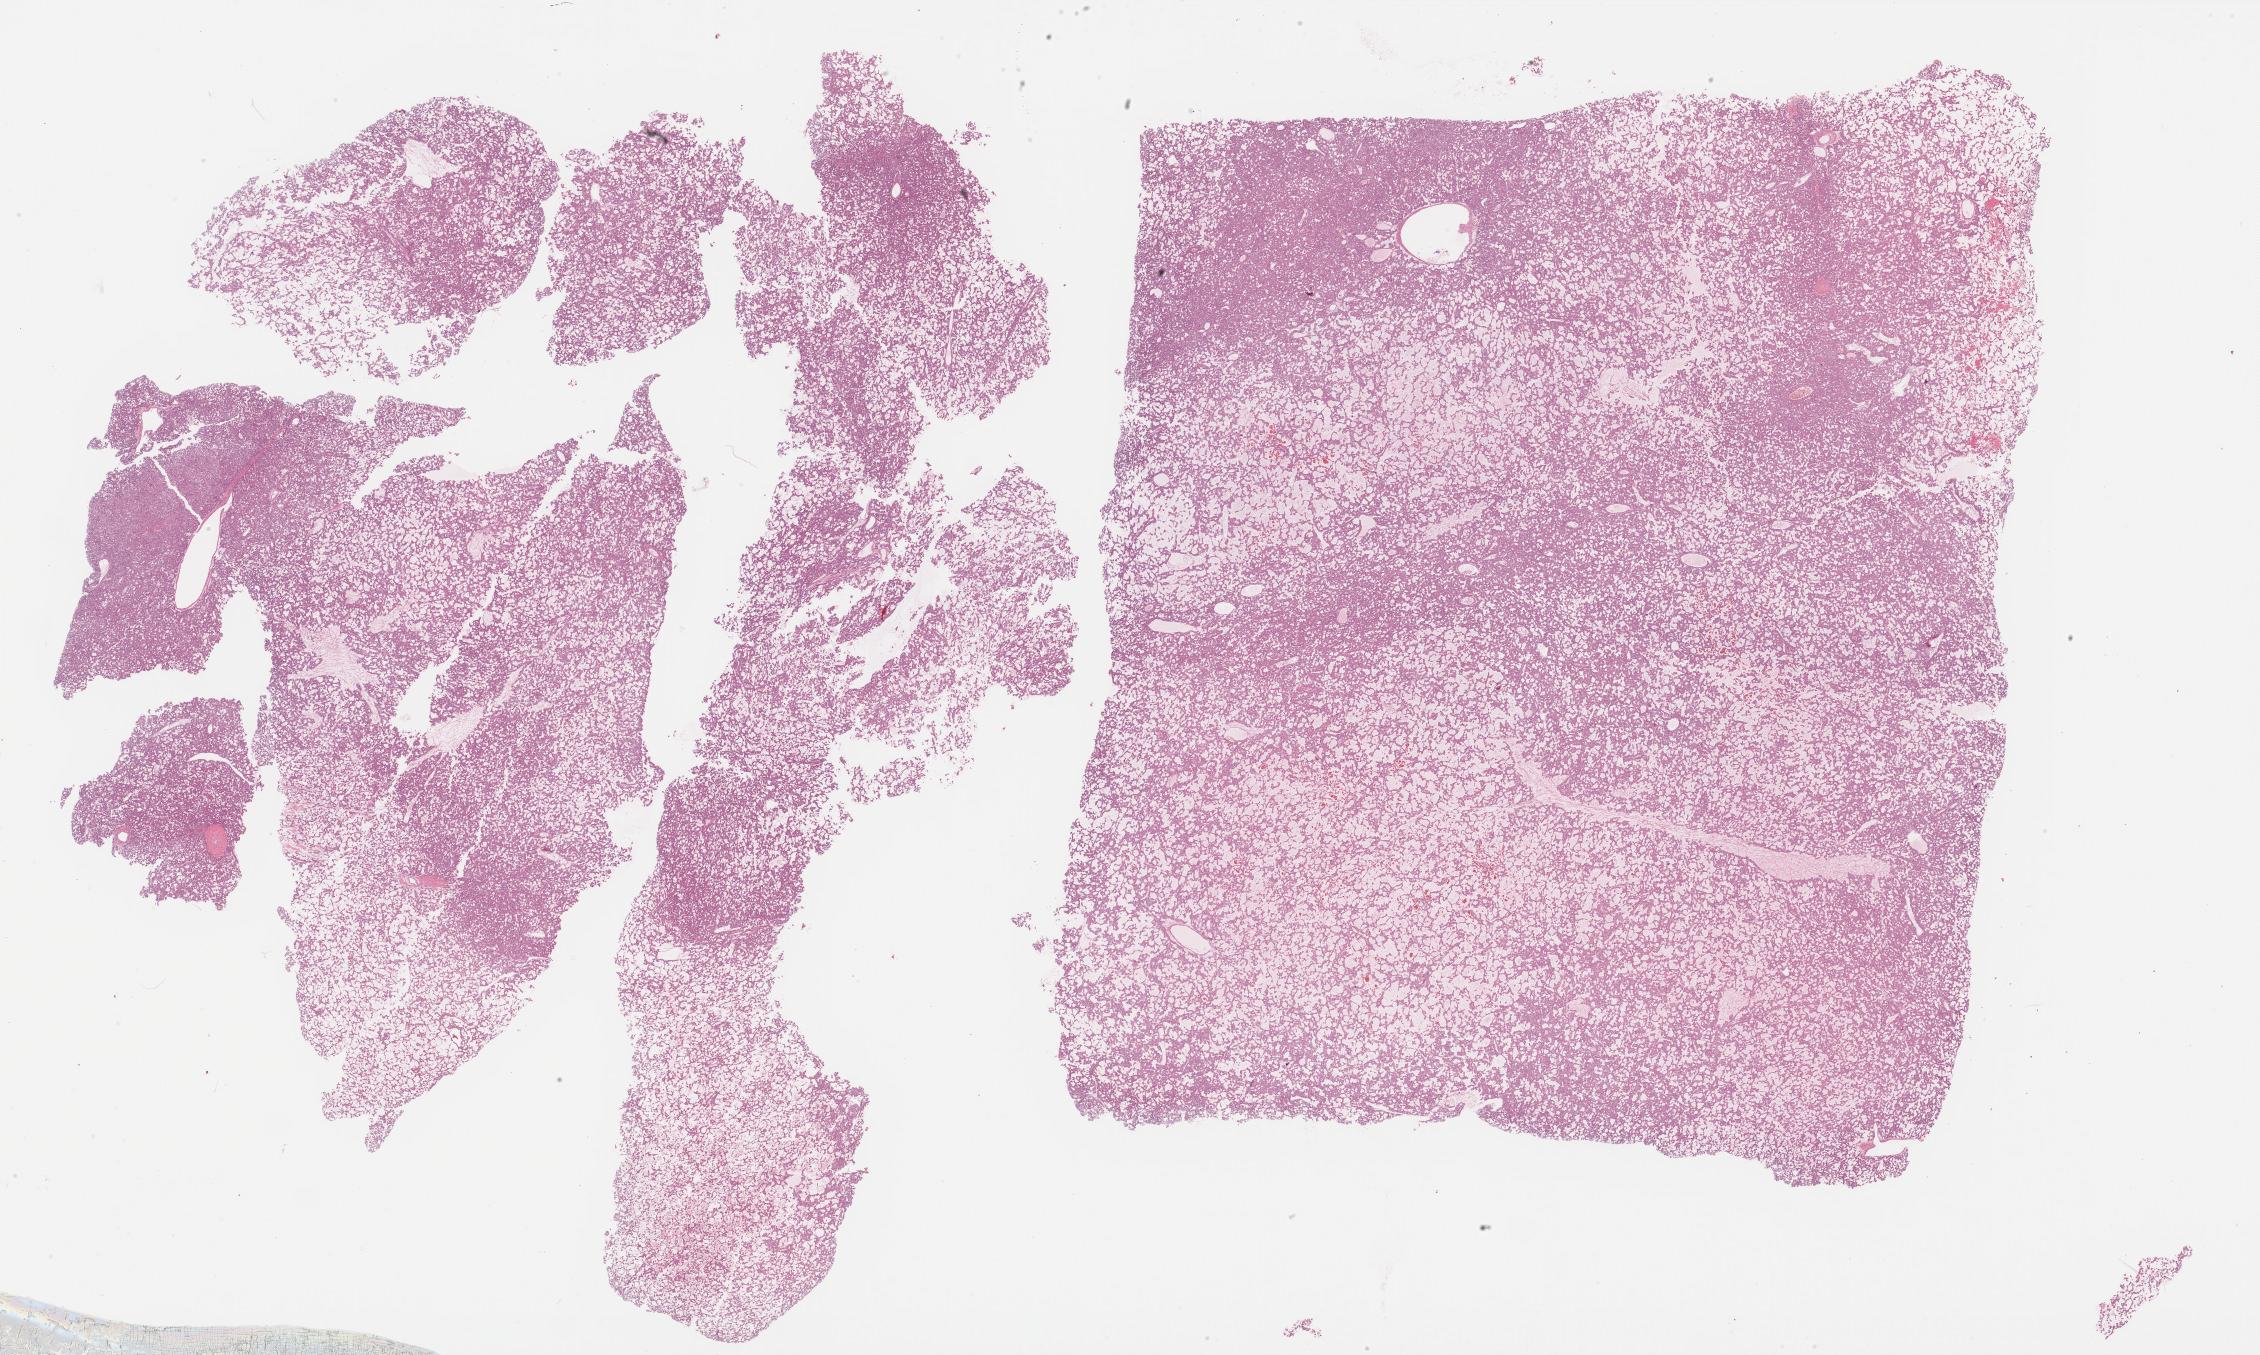
Hematoxylin and eosin (H&E) stained whole-slide image, a low-resolution overview of the entire scanned area, about 36.6 x 21.9 mm (slide scanned at 40x), FFPE section, primary tumour sample from the liver. Patient: female, age at initial diagnosis 65 years. Histologic grade: G1 (well differentiated).
AJCC pathologic stage: IIIA (7th edition). Diagnosis: Hepatocellular carcinoma, NOS.